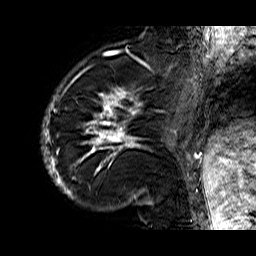
Breast MRI (dynamic contrast-enhanced), one sagittal slice. Position 13 of 60 along the scan axis. Dynamic contrast-enhanced series, time point 2 of 6 at this slice position (early post-contrast). 1.5 T. TE 6.3 ms, TR 32.9 ms. 4 mm slice thickness. 256 × 256 image matrix, field of view 200 × 200 mm. Female patient. From the clinical record (not read from this slice): setting: breast cancer imaged before/during neoadjuvant chemotherapy; receptor status: HR-positive, HER2-negative.
Structures marked on this image (semi-automatic segmentation, software-assisted and operator-edited):
- analysis volume of interest (the breast-tissue region the enhancement analysis was run in; not a lesion): bounding box [x1, y1, x2, y2] px = [41, 74, 176, 210]
- tumour enhancement mask (voxels above the 100 % enhancement threshold inside the analysis volume of interest): [42, 74, 176, 205]